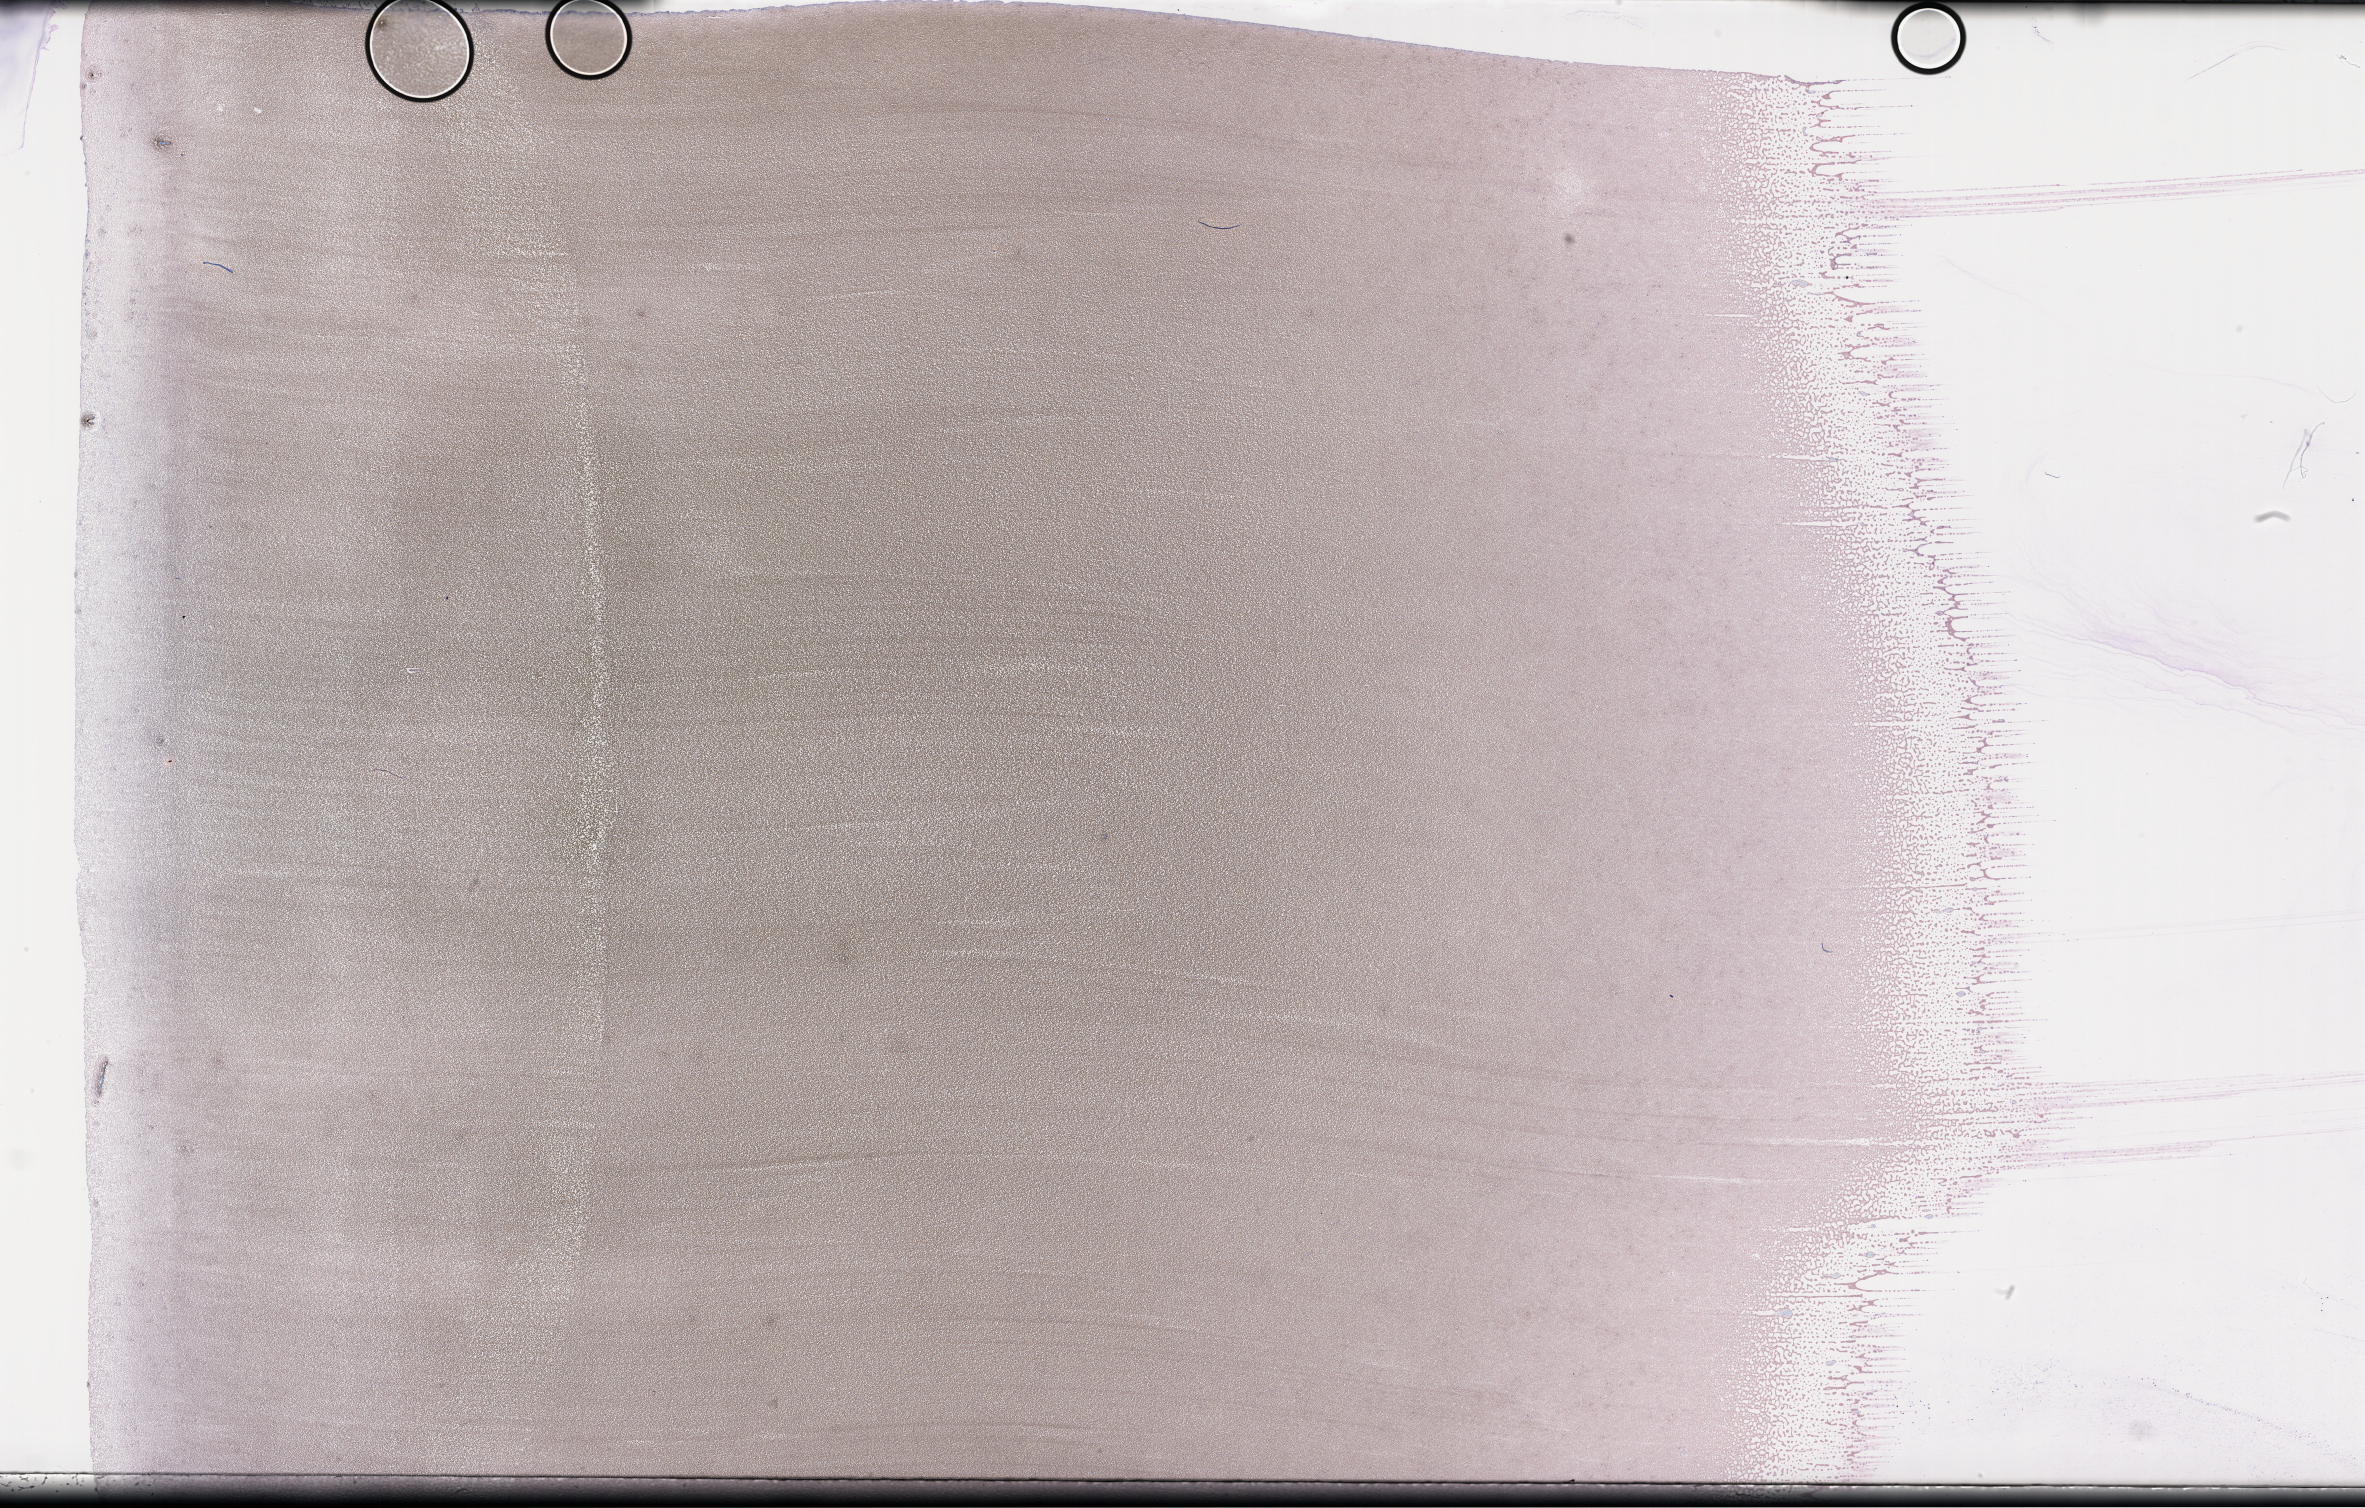
Wright–Giemsa-stained whole blood smear, whole-slide image — whole scanned area (about 38.2 x 24.4 mm) shown as a low-resolution overview. EDTA-anticoagulated smear. Patient sex: male.
• from a patient with: Plasma Cell Myeloma